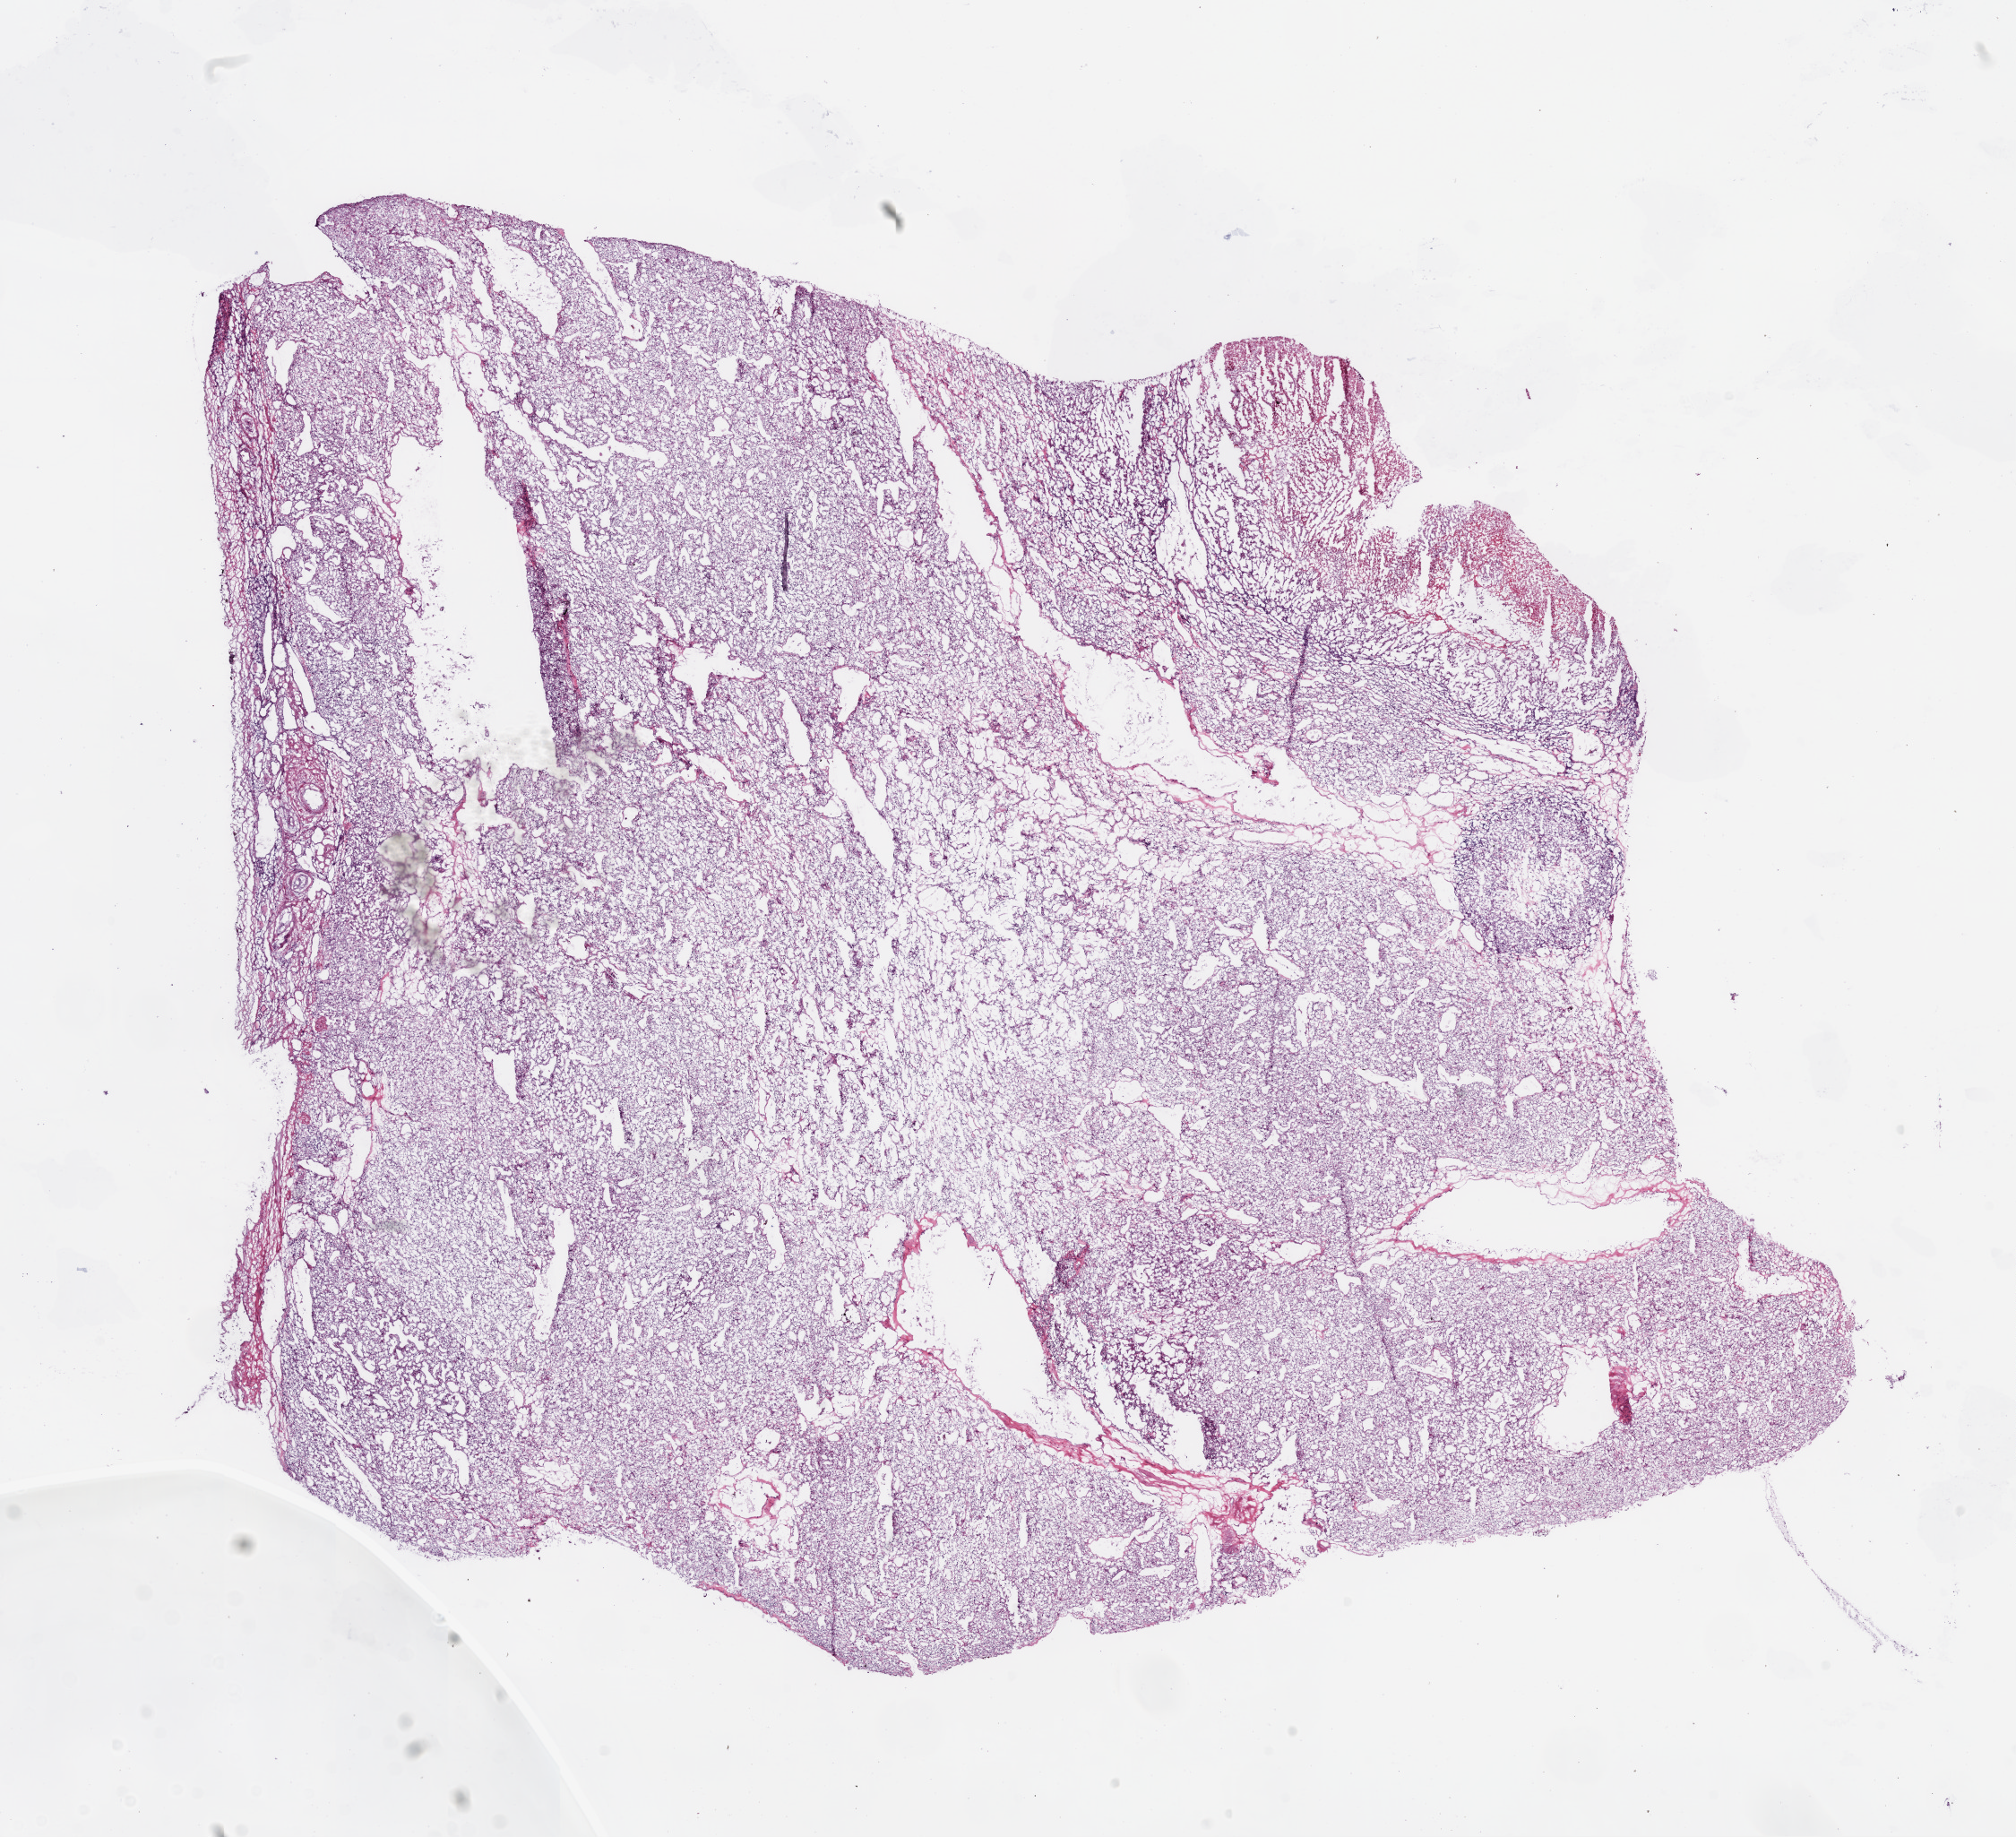
Whole-slide histology image, H&E, low-resolution overview of the scanned area, about 18.1 x 16.4 mm (acquisition: 20x scan), frozen section from the bottom of the tissue portion, sample: primary tumour, kidney. Patient: female, age at initial diagnosis 65 years. Histologic grade: G3 (poorly differentiated). Pathologist review of this section (percent, as recorded): tumour cells 85%, tumour nuclei 80%, normal cells 0%, stromal cells 10%, necrosis 5%.
Diagnosis: Clear cell adenocarcinoma, NOS. AJCC pathologic stage: IV.